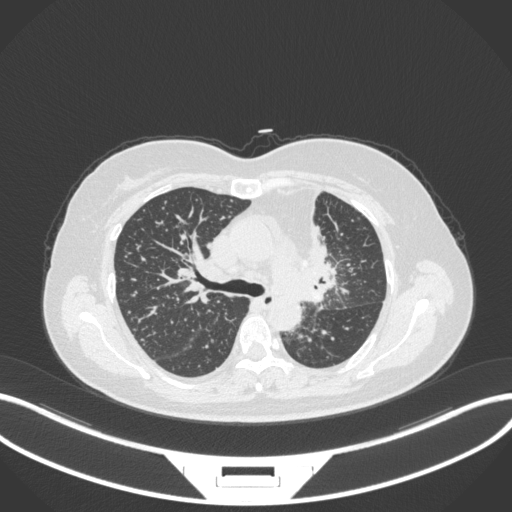
Chest CT, one axial slice. Slice 218 of 348 in the series (ordered by position). Reconstruction kernel B31f. 120 kVp. Lung window (W 1500 / L -600 HU). 512 × 512 image matrix, field of view 400 × 400 mm. Patient: female, 49 years. Case-level facts recorded for this patient, not image findings: clinical TNM (as recorded): T1c N0 M1.
Structures marked on this image (rectangle marked by the reading radiologist):
- lung tumour (recorded histology: adenocarcinoma): bounding box (x1, y1, x2, y2) in pixels: (298, 182, 335, 306)